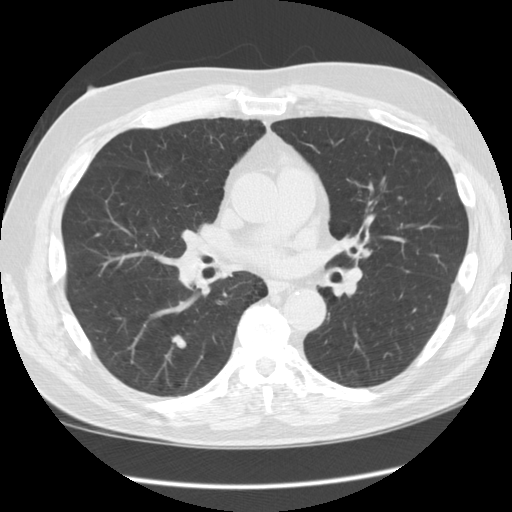
Axial slice from a low-dose chest CT screening exam; third annual screen; lung window (W 1500 / L -600 HU); 2.5 mm slice thickness; 512 × 512 image matrix, field of view 360 × 360 mm. Male participant, aged 60 years at enrolment. Former smoker at enrolment.
Expert-annotated lung lesion, bounding box (x1, y1, x2, y2) in pixels: (153, 328, 193, 361). The screening reader recorded 5 non-calcified nodules or masses ≥4 mm on this exam (right middle lobe, right upper lobe, left upper lobe, left lower lobe, right upper lobe); which of them this box marks is not recorded. Later outcome: lung cancer diagnosed 353 days after this screen — squamous cell carcinoma, clear cell type, right lower lobe, stage IV (AJCC 6th edition), 12 mm at pathology.